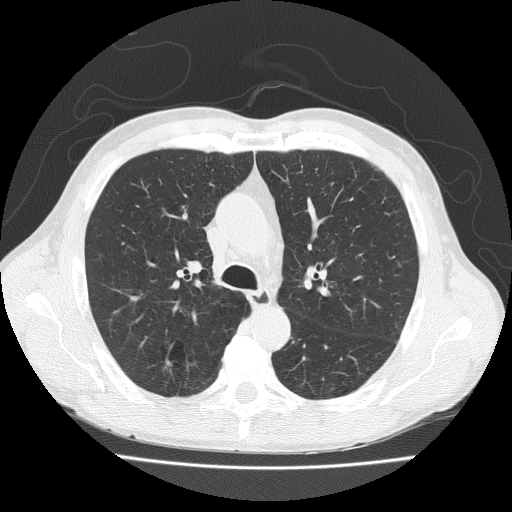
Chest CT (low-dose screening protocol), one axial image; baseline annual screen; lung window (W 1500 / L -600 HU); 2 mm slice thickness; 120 kVp; slice 68 of 203 in the series; 512 × 512 image matrix, field of view 370 × 370 mm. Male, age 73 years at enrolment. Current smoker at enrolment.
Expert-annotated lung lesion, bounding box [x1, y1, x2, y2] px = [145, 339, 198, 387]. Screening reader's record for this exam: no non-calcified nodule ≥4 mm recorded. Participant outcome: lung cancer diagnosed 777 days after this screen (after the third annual screen) — adenosquamous carcinoma, right upper lobe, well differentiated (G1), stage IA (AJCC 6th edition), 20 mm at pathology.